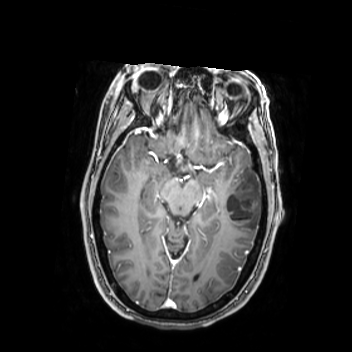
Brain MRI from a brain-tumour surgery series, one axial slice. T1-weighted post-contrast. 0.9 mm slice thickness. 352 × 352 image matrix, field of view 280 × 280 mm. From the clinical record (not read from this slice): histopathology: Oligodendroglioma; WHO grade: 2; IDH mutation: yes.
Structures marked on this image (manually delineated by an expert):
- tumour: bounding box [x1, y1, x2, y2] px = [224, 167, 262, 233]